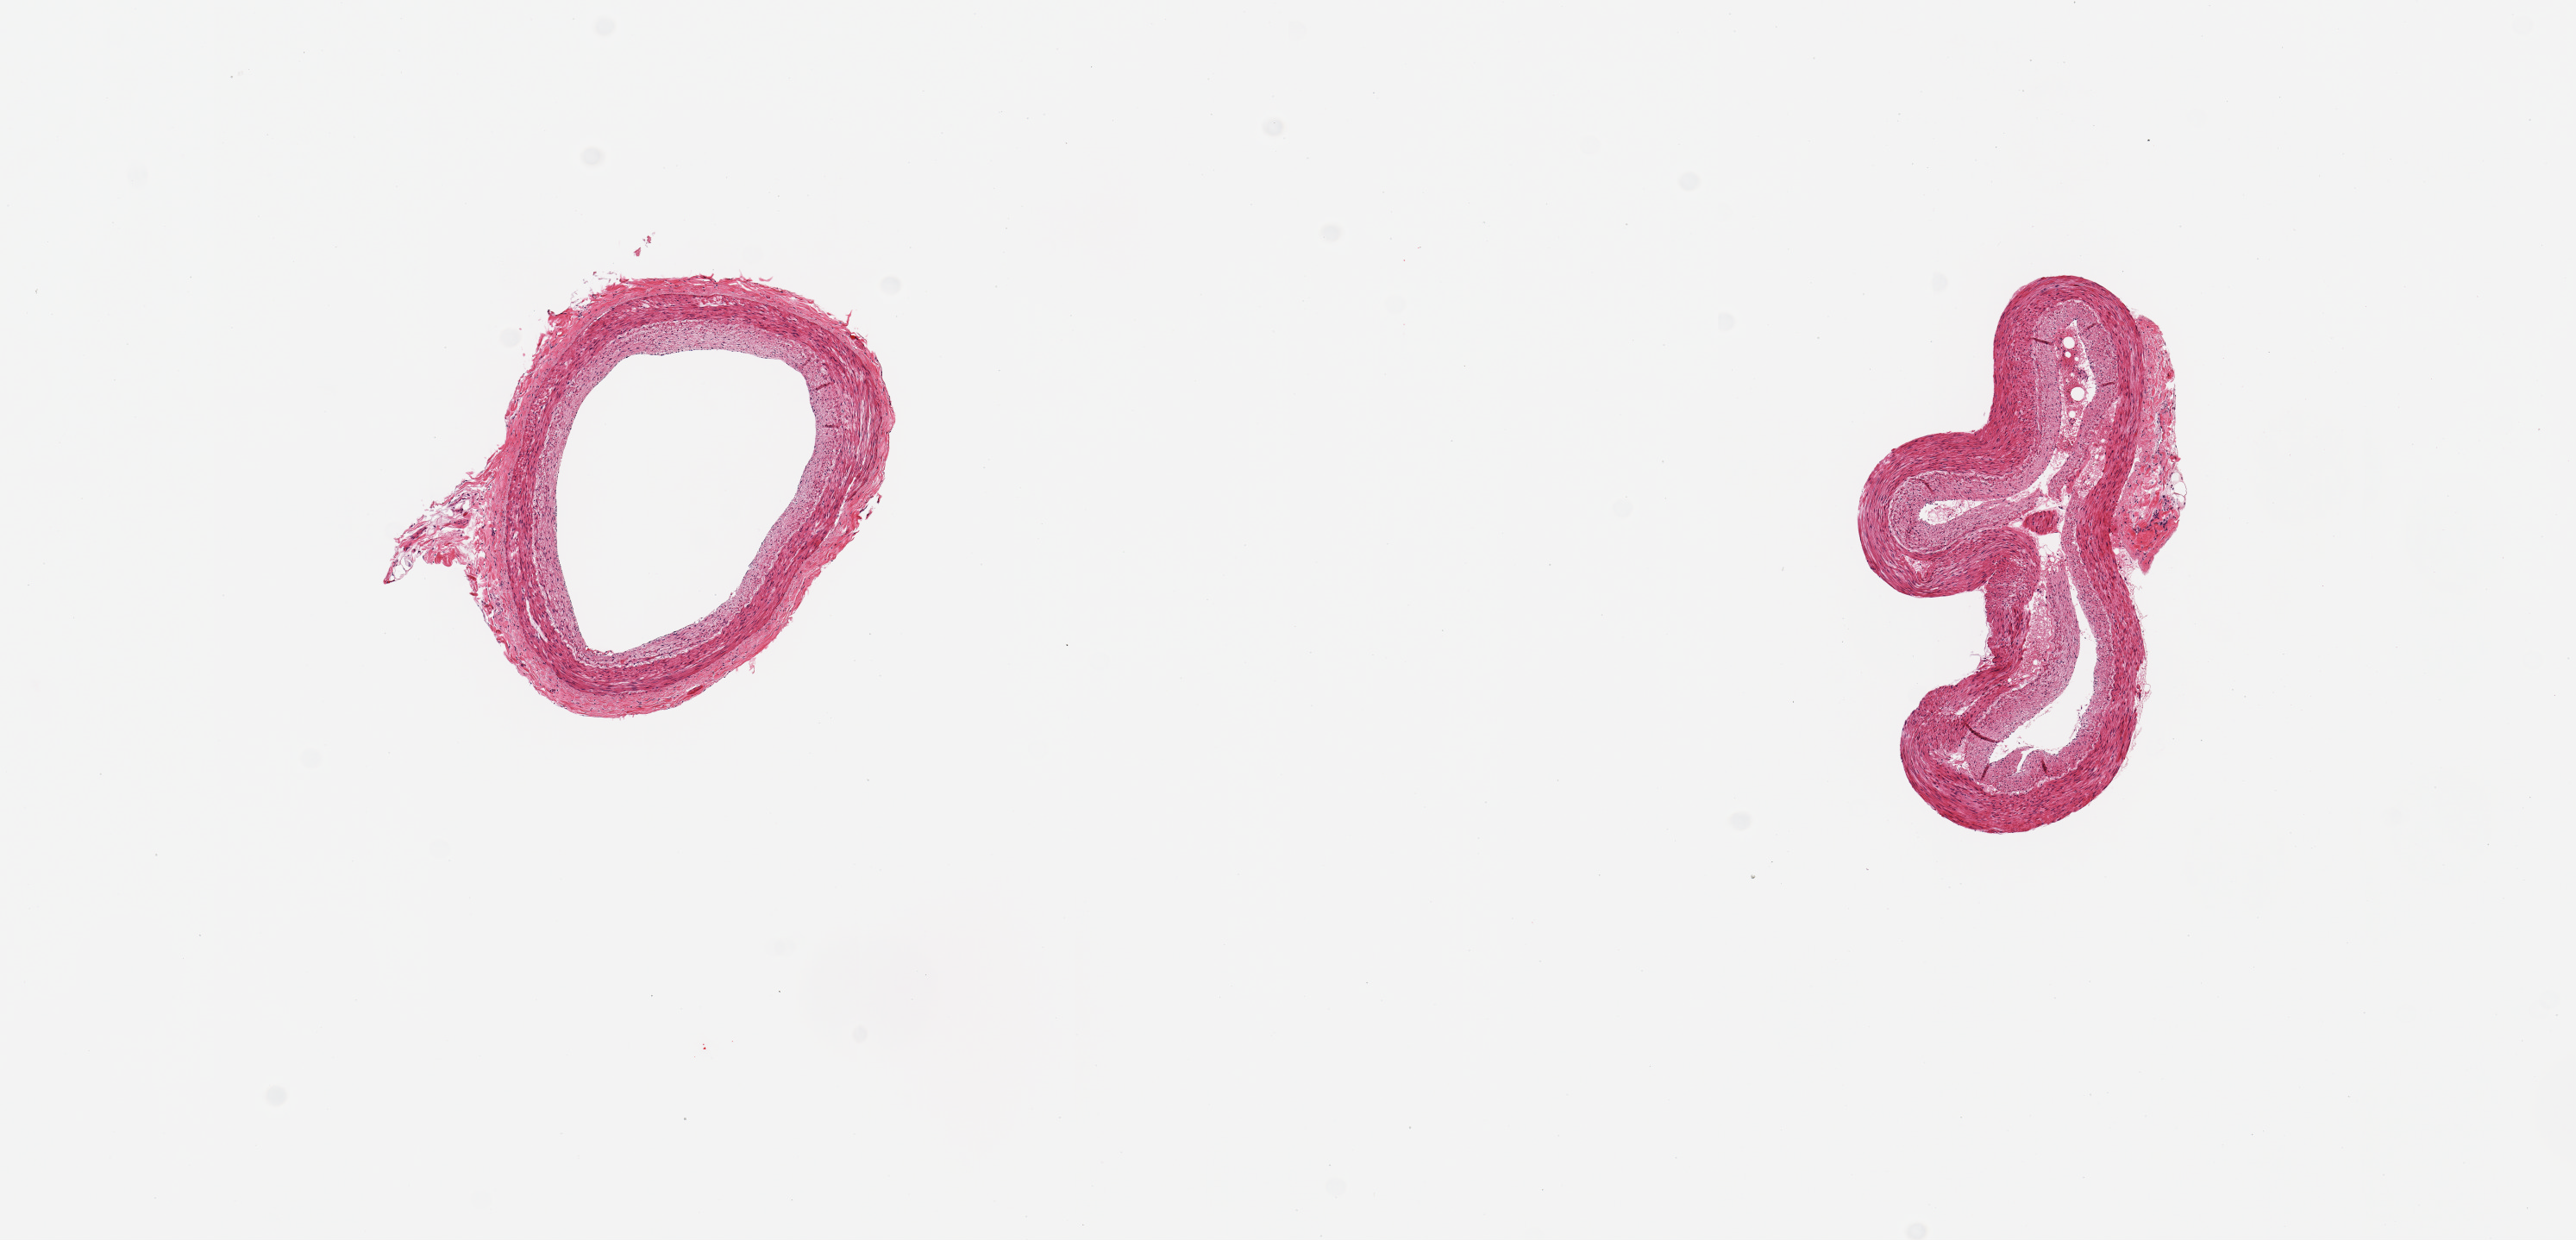
Digitized haematoxylin and eosin-stained section, brightfield, a low-resolution overview of the entire scanned area, about 11.8 x 5.7 mm; PAXgene-fixed paraffin-embedded (PFPE) section; sampled site (target tissue): coronary artery; tissue donor sample. Female donor.
Reviewer comment on this tissue sample: 2 pieces; no lesions; well trimmed.